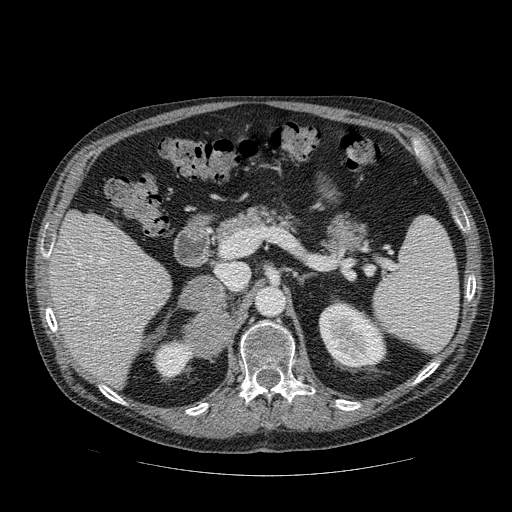
Contrast-enhanced abdominal CT, one axial slice; reconstruction kernel STANDARD; 120 kVp; soft-tissue window (W 400 / L 40 HU); 2.5 mm slice thickness; 512 × 512 image matrix, field of view 420 × 420 mm. Male patient, age 56 years. Case-level facts recorded for this patient, not image findings: diagnosis: adrenocortical carcinoma; tumour side: right adrenal; tumour size at pathology: 9 cm; Ki-67 index: 48 %; stage (as recorded): 4.
Outlined on this slice (semi-automatic segmentation, software-assisted and operator-edited):
- mass: bounding box (x1, y1, x2, y2) in pixels: (180, 276, 233, 353)